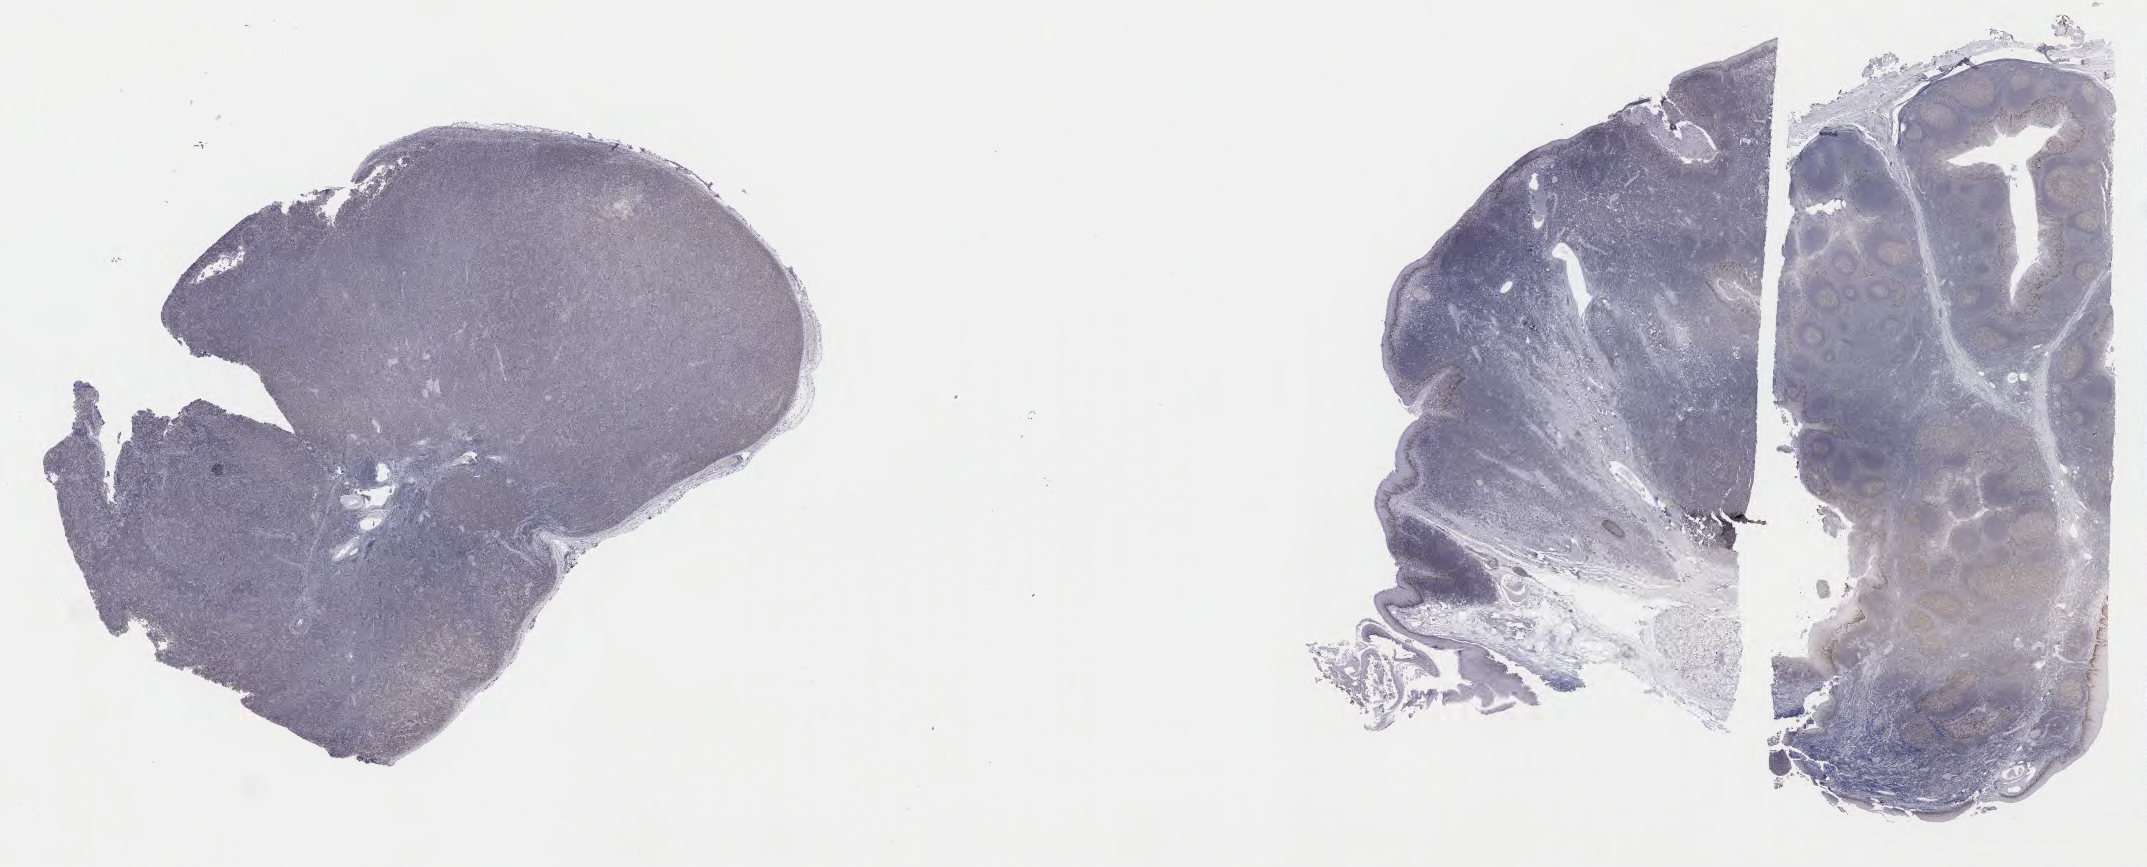
IHC for p53, whole-slide image — whole scanned area (about 34.7 x 14.0 mm) shown as a low-resolution overview. Tumor tissue. Site: lymph node. Patient male; 32 years old.
Diagnosis: Diffuse large B-cell lymphoma, NOS.